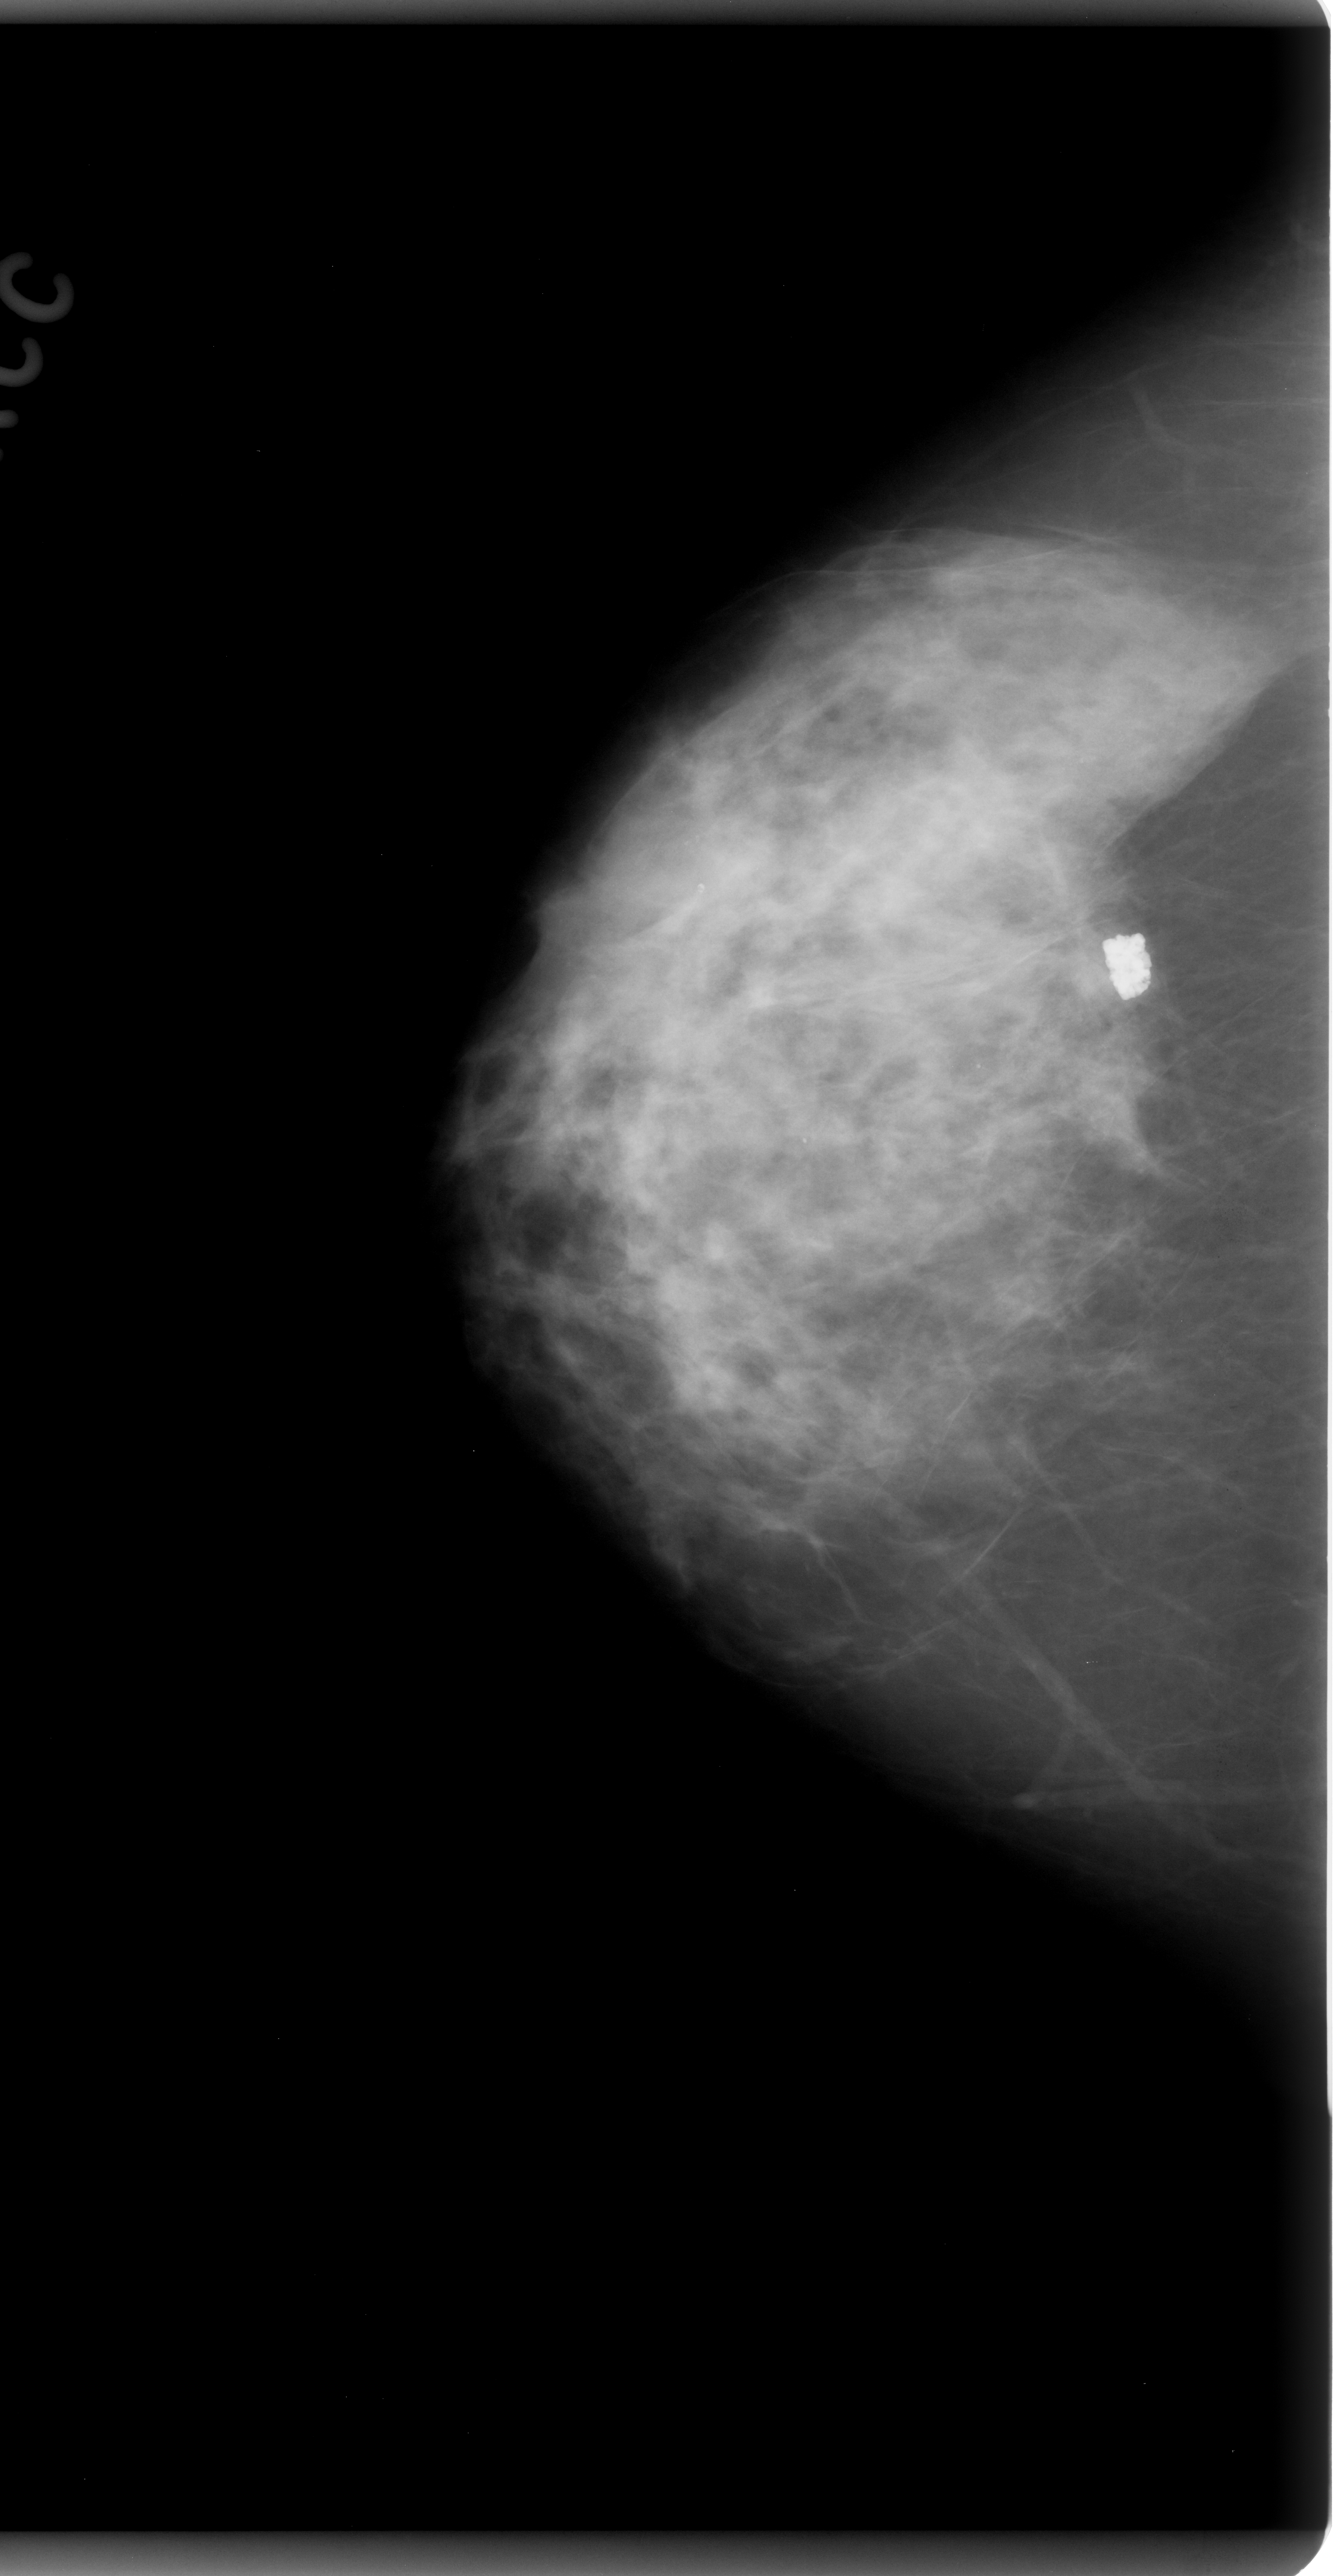
Scanned film-screen mammogram; right breast; CC view; 1337 × 2576 image matrix.
Expert-marked regions of interest on this image (one box per marked abnormality):
- mass, shape irregular, margins spiculated; BI-RADS assessment category 5; subtlety rating 4 on a 1 (subtle) to 5 (obvious) scale; pathology (as recorded): malignant: box from (x=983, y=847) to (x=1158, y=1004) px